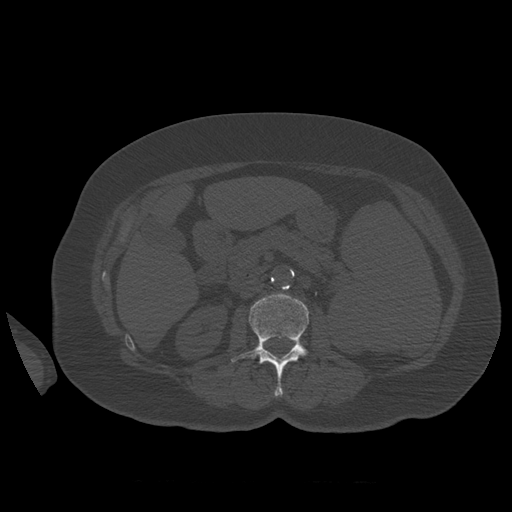
CT including the spine, one axial slice. Slice 253 of 399 in the series (ordered by position). Reconstruction kernel STANDARD. 120 kVp. Bone window (W 1800 / L 400 HU). 1.25 mm slice thickness. 512 × 512 image matrix. Patient age 81 years. Case-level facts recorded for this patient, not image findings: primary cancer: renal; vertebrae with lytic lesions (as recorded): L1.
Annotated regions visible in this slice (semi-automatically segmented with operator editing):
- L2 vertebra: bounding box <231,294,309,397> (left, top, right, bottom; pixels)